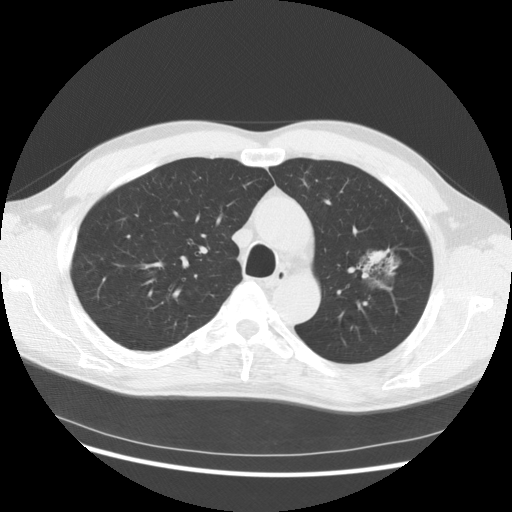
Low-dose screening chest CT, one axial slice. Position 101 of 145 along the scan axis. Lung window (W 1500 / L -600 HU). 2.5 mm slice thickness. 512 × 512 image matrix, field of view 370 × 370 mm.
Annotated regions visible in this slice (outlined manually by an expert reader):
- lesion 1 (tumor, upper lobe of left lung): bounding box <364,250,395,273> (left, top, right, bottom; pixels)